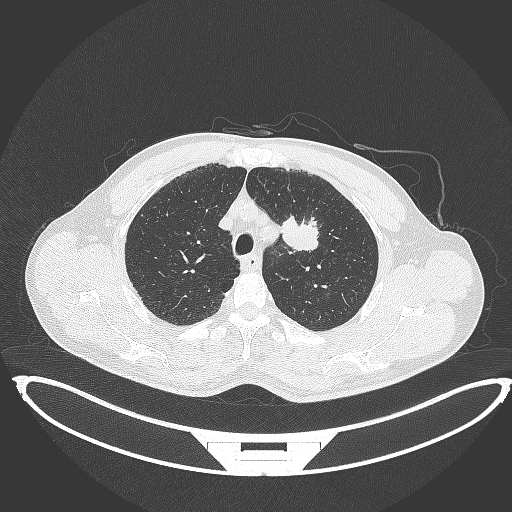
Chest CT, one axial slice. Slice 344 of 395 in the series (ordered by position). Reconstruction kernel B70f. 120 kVp. Lung window (W 1500 / L -600 HU). 512 × 512 image matrix, field of view 457 × 457 mm. Patient: male, 60 years. From the clinical record (not read from this slice): clinical TNM (as recorded): T2a N0 M0.
Annotated regions visible in this slice (bounding box drawn by a radiologist):
- lung tumour (recorded histology: squamous cell carcinoma): bounding box <275,210,324,255> (left, top, right, bottom; pixels)